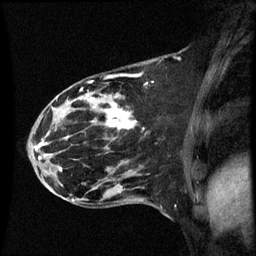
Breast MRI (dynamic contrast-enhanced), one sagittal slice; position 22 of 60 along the scan axis; dynamic contrast-enhanced series, image 2 of 3 at this slice position (ordered by acquisition); 1.5 T; TE 4.2 ms, TR 8.9 ms; 2 mm slice thickness; 256 × 256 image matrix, field of view 200 × 200 mm. Female patient, age 44 years. Case-level facts recorded for this patient, not image findings: setting: breast cancer imaged before/during neoadjuvant chemotherapy; receptor status: HR-positive, HER2-negative.
Structures marked on this image (semi-automatic segmentation, software-assisted and operator-edited):
- analysis volume of interest (the breast-tissue region the enhancement analysis was run in; not a lesion): bounding box <43,80,147,189> (left, top, right, bottom; pixels)
- tumour enhancement mask (voxels above the 70 % enhancement threshold inside the analysis volume of interest): <107,106,136,129>